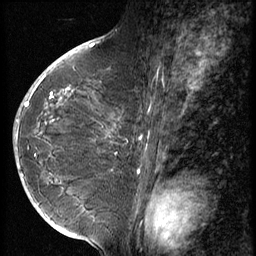
Breast MRI (dynamic contrast-enhanced), one sagittal slice; 3 images stored at this slice position (order not interpretable as contrast timing); 1.5 T; TE 4.2 ms, TR 9 ms; 2.5 mm slice thickness; 256 × 256 image matrix, field of view 180 × 180 mm. Female patient, age 49 years. Case-level facts recorded for this patient, not image findings: setting: breast cancer imaged before/during neoadjuvant chemotherapy; receptor status: HER2-positive.
Structures marked on this image (semi-automatic segmentation, software-assisted and operator-edited):
- analysis volume of interest (the breast-tissue region the enhancement analysis was run in; not a lesion): bounding box [x1, y1, x2, y2] px = [13, 79, 110, 203]
- tumour enhancement mask (voxels above the 140 % enhancement threshold inside the analysis volume of interest): [15, 133, 23, 175]